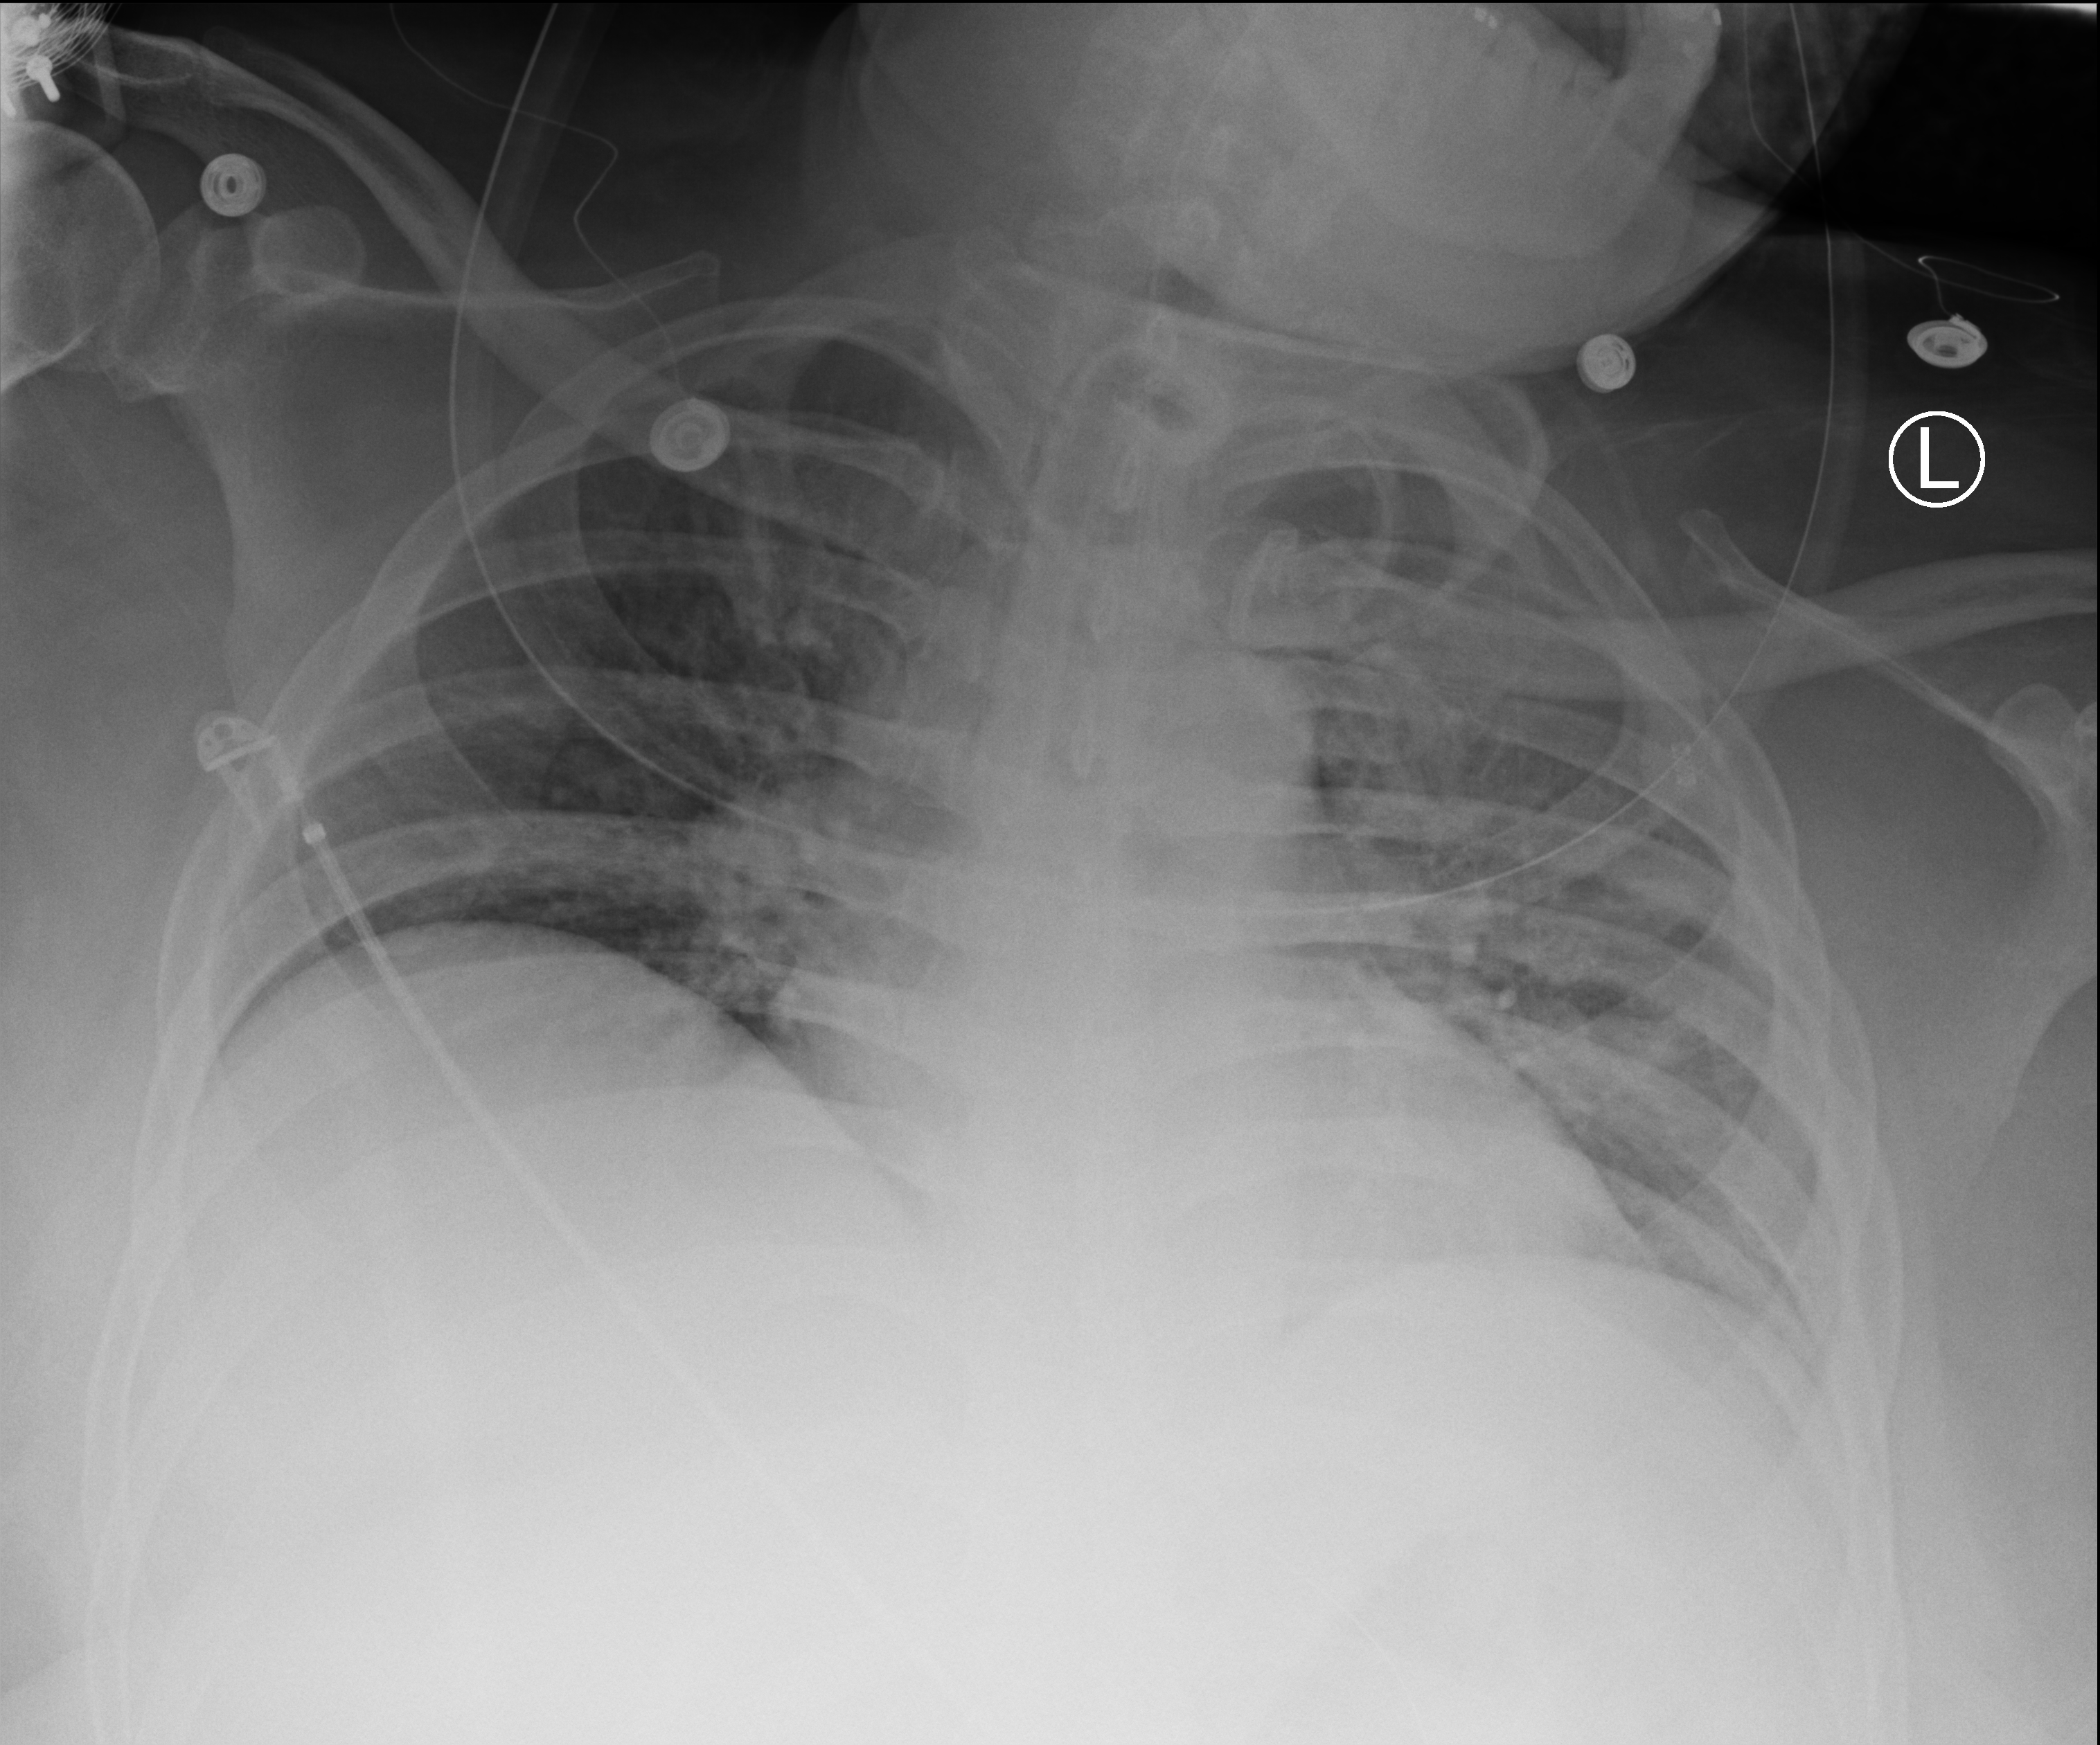
Chest X-ray (portable), anteroposterior (AP) projection. Patient hospitalised with COVID-19; male, aged 18–59 years.
Admission-level facts for this patient (not findings on this image; timing relative to this image not recorded):
- mechanically ventilated during this hospital stay: yes